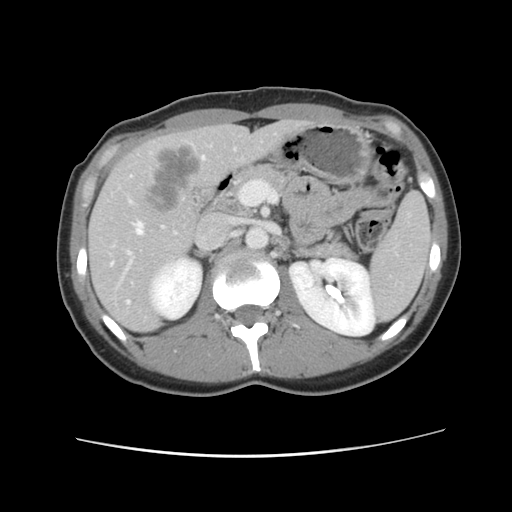
Contrast-enhanced abdominal CT, one axial slice; slice 54 of 134 in the series (ordered by position); 120 kVp; intravenous contrast given; soft-tissue window (W 400 / L 40 HU); 2.5 mm slice thickness; 512 × 512 image matrix, field of view 339 × 339 mm. Female patient, age 33 years. Case-level facts recorded for this patient, not image findings: diagnosis: colorectal cancer liver metastases, imaged before liver resection; multiple liver metastases: yes; largest metastasis: 4.5 cm; disease in both lobes: yes.
Outlined on this slice (expert manual segmentation):
- hepatic veins: bounding box (x1, y1, x2, y2) in pixels: (112, 156, 206, 303)
- liver: (90, 121, 307, 331)
- planned liver remnant (the part of the liver to remain after resection): (91, 121, 305, 332)
- portal vein (with intrahepatic branches): (115, 225, 178, 290)
- liver metastasis: (141, 143, 200, 211)